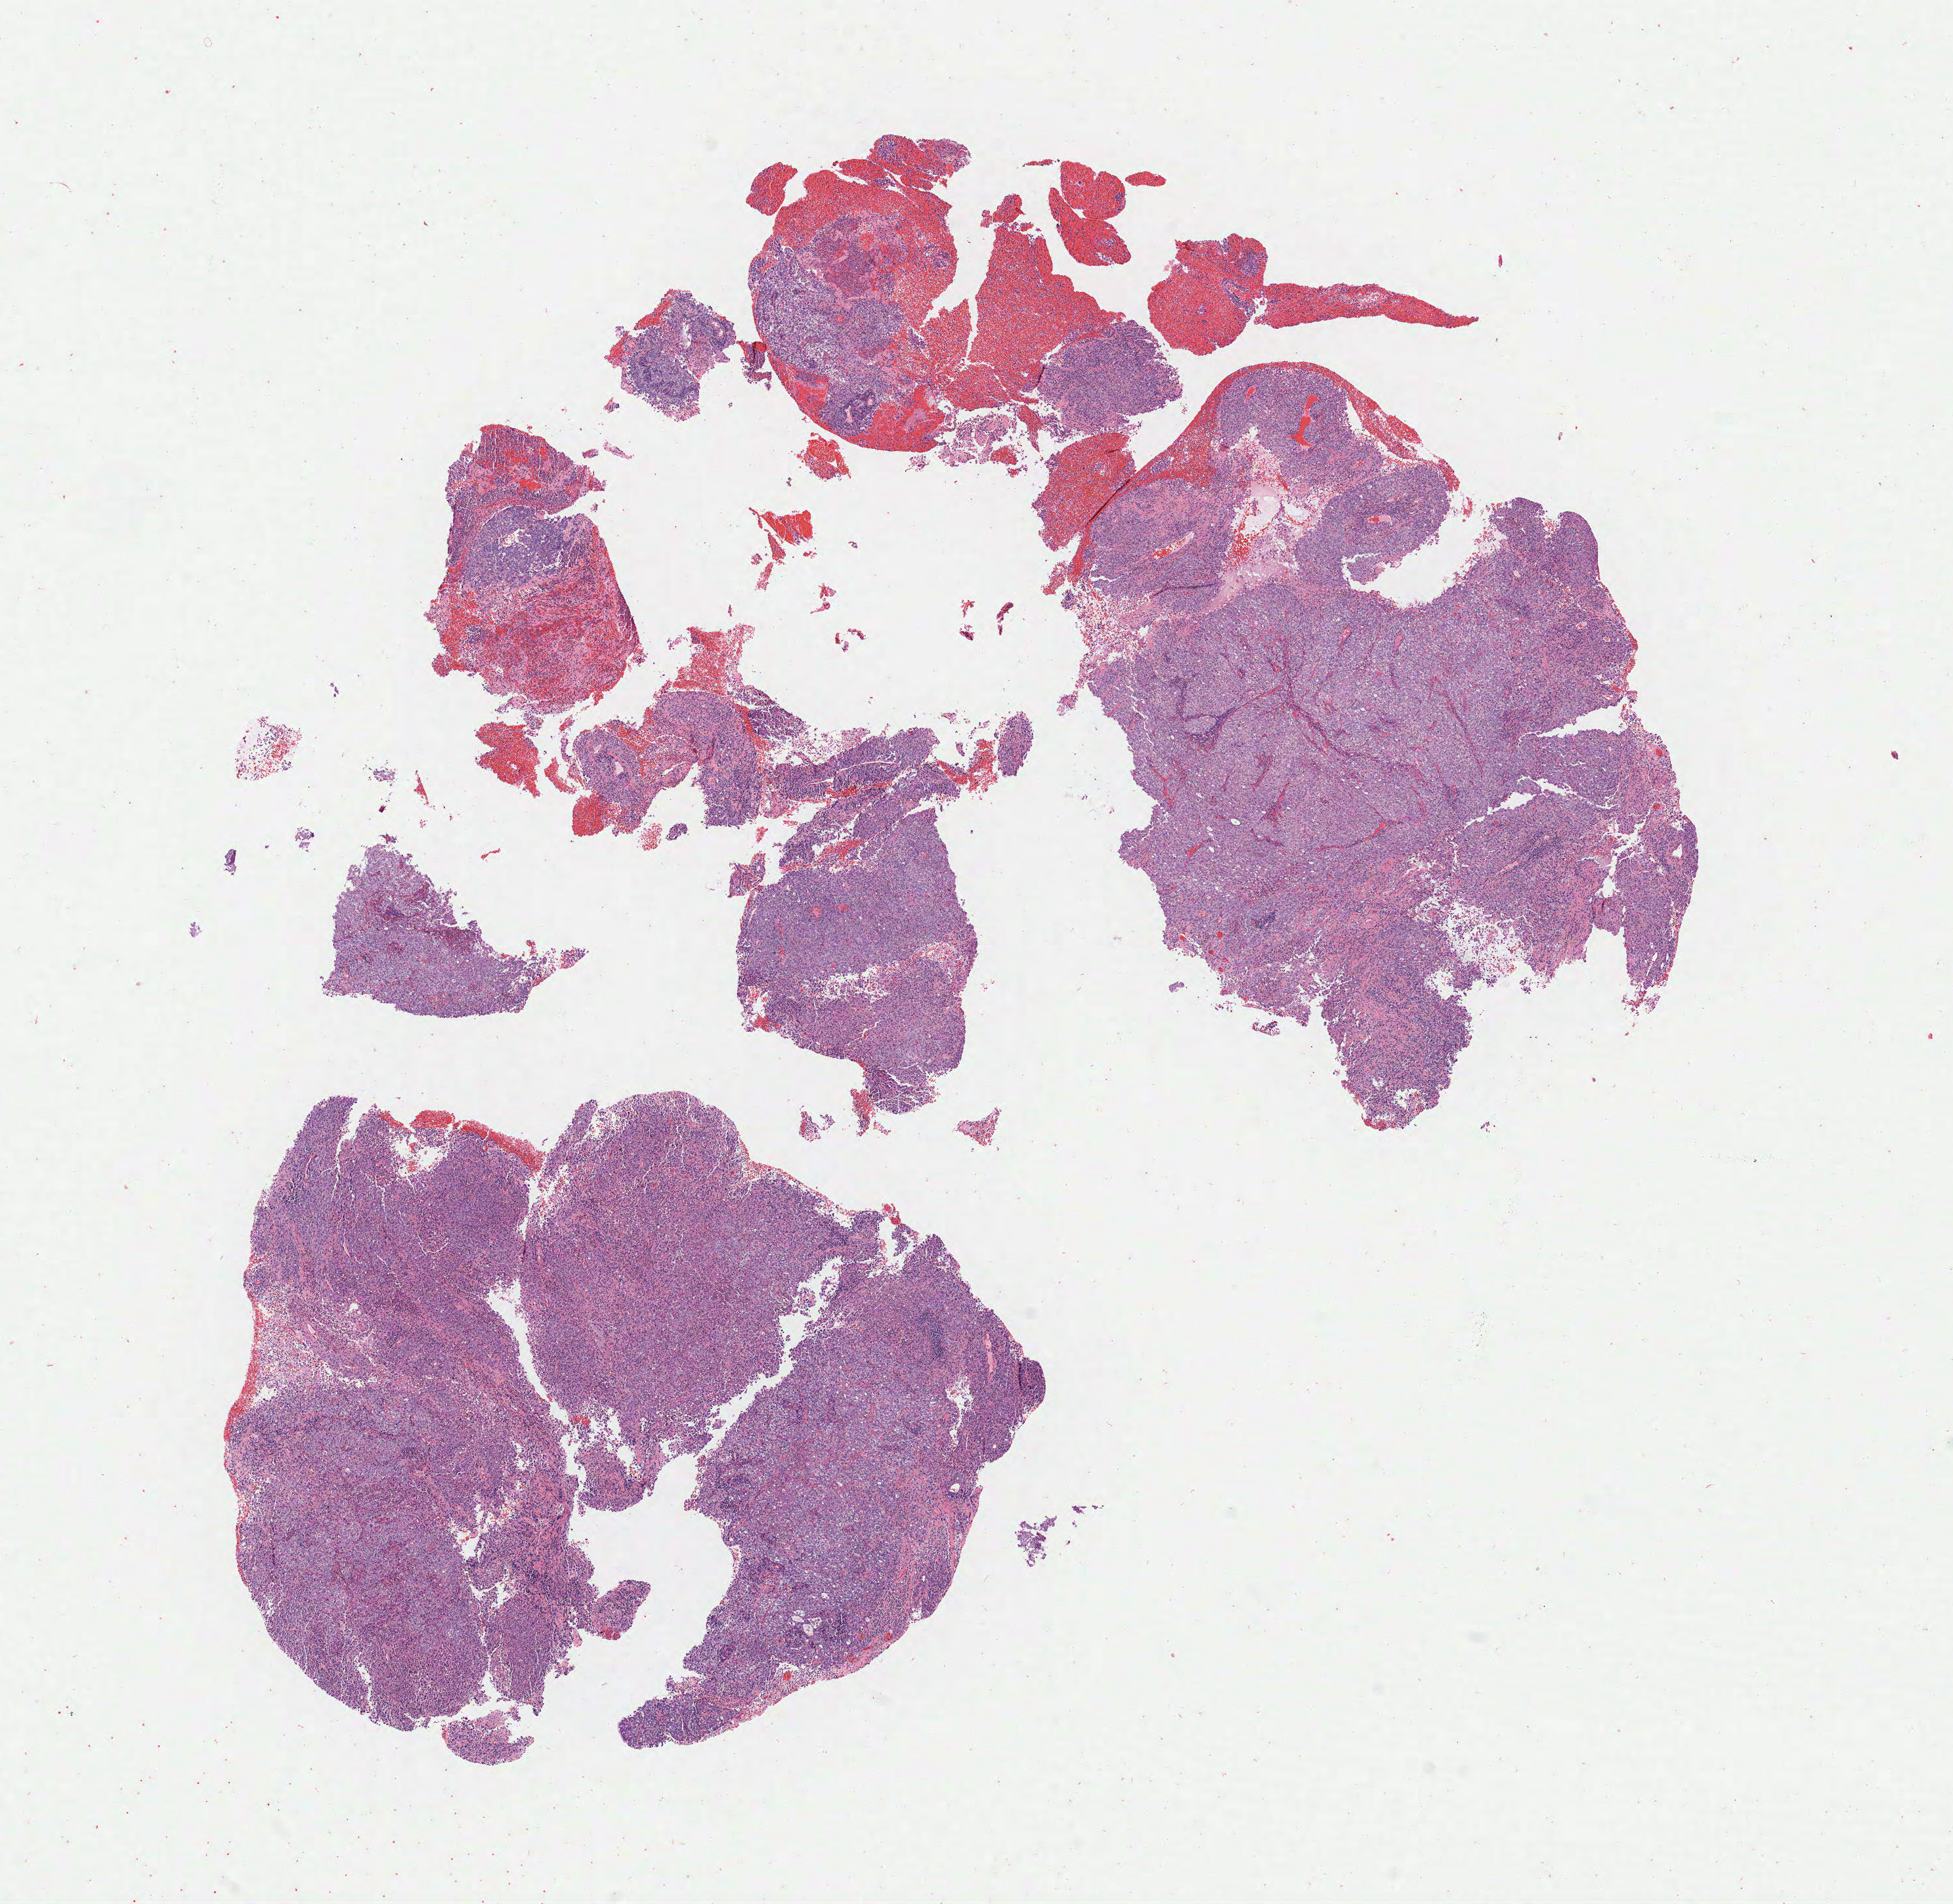
Hematoxylin and eosin (H&E) whole-slide image — low-resolution overview of the scanned area, about 11.8 x 11.5 mm; tumor tissue; site: cervix. Female patient, age 70 years.
Diagnosis: Squamous cell carcinoma, large cell, nonkeratinizing, NOS.